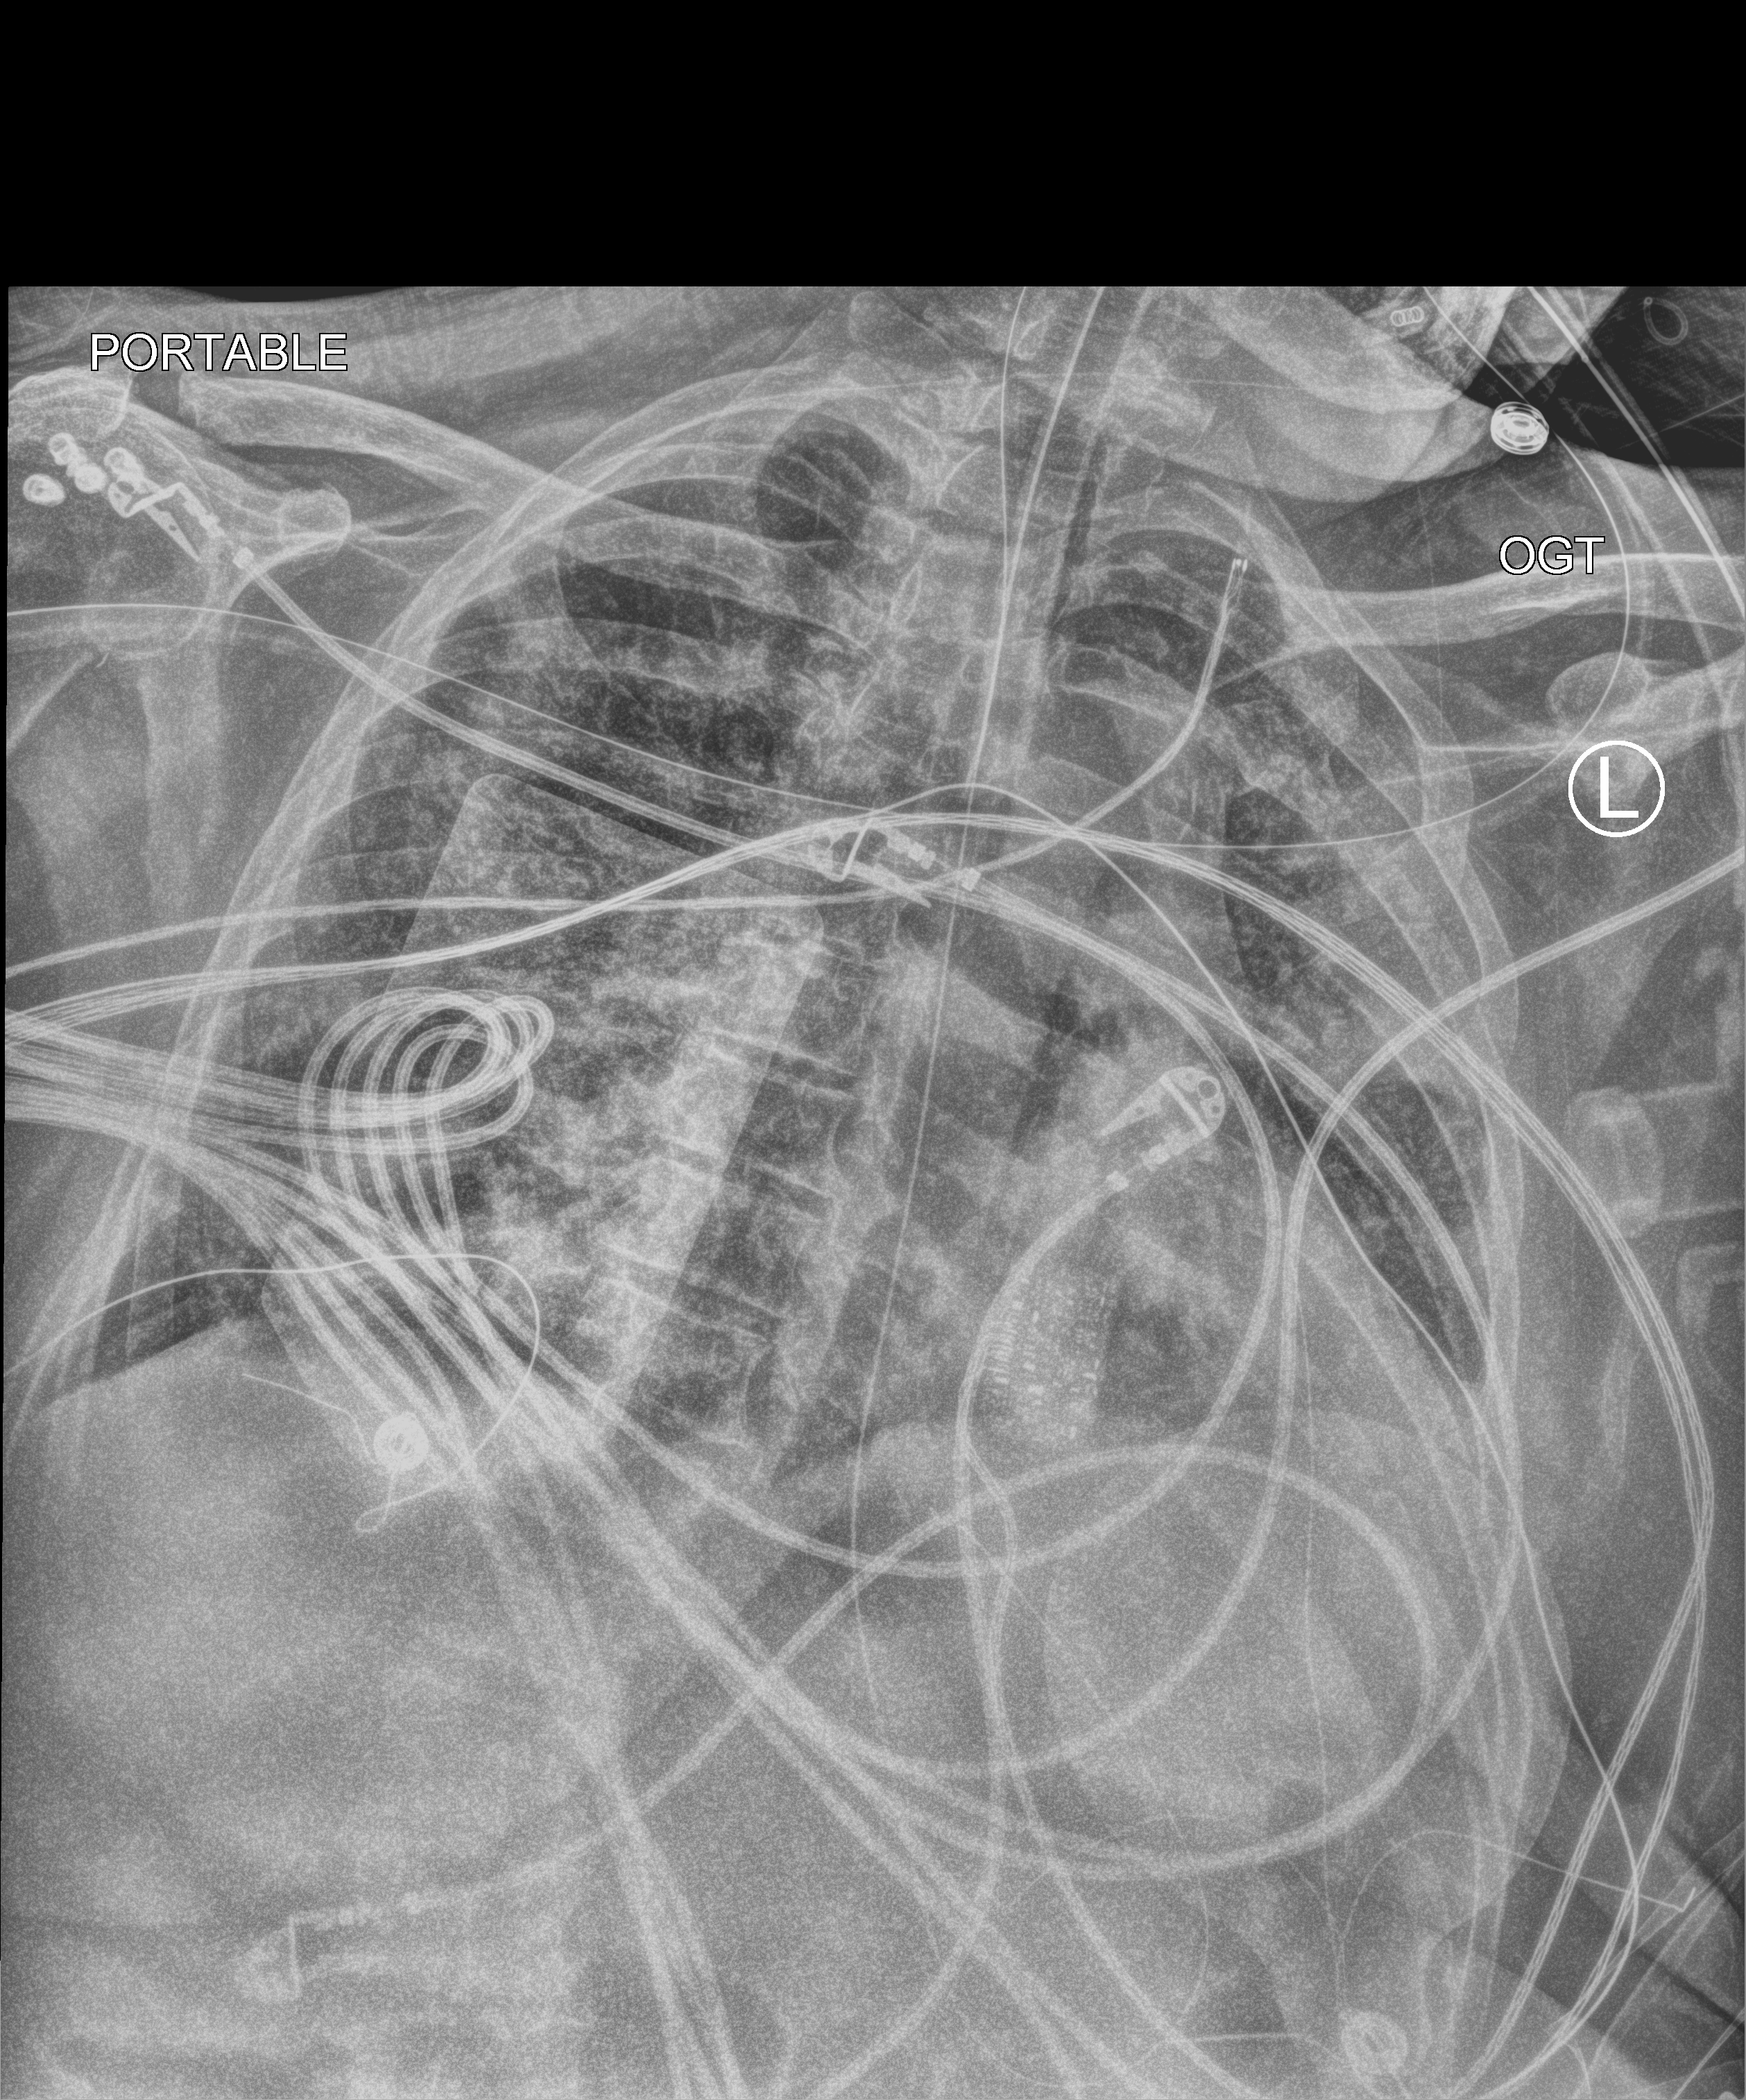
Portable chest radiograph, anteroposterior (AP) projection. Patient hospitalised with COVID-19; female, aged 60–74 years.
Hospital-stay facts (about this admission, not read from this image; timing relative to this image not recorded): mechanically ventilated during this hospital stay: yes; admitted to intensive care during this hospital stay: yes.